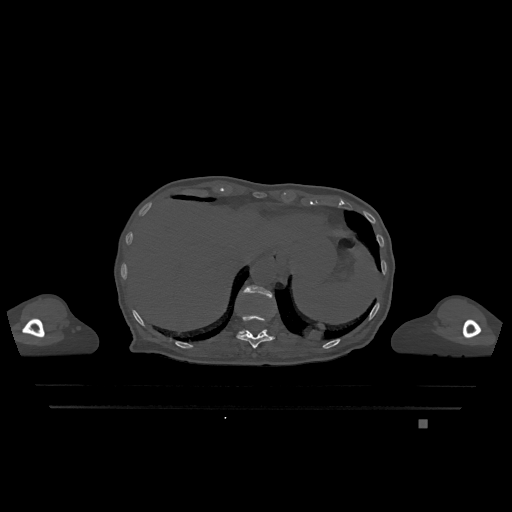
CT including the spine, one axial slice; slice 575 of 1317 in the series (ordered by position); bone window (W 1800 / L 400 HU); 512 × 512 image matrix, field of view 500 × 500 mm. Female patient, age 74 years. From the clinical record (not read from this slice): primary cancer: lung; vertebrae with lytic lesions (as recorded): T1, T4, T5, T6, L4, L5.
Outlined on this slice (semi-automatic segmentation, software-assisted and operator-edited):
- T11 vertebra: box from (x=236, y=314) to (x=275, y=348) px
- T12 vertebra: (x=239, y=285)–(x=272, y=334)